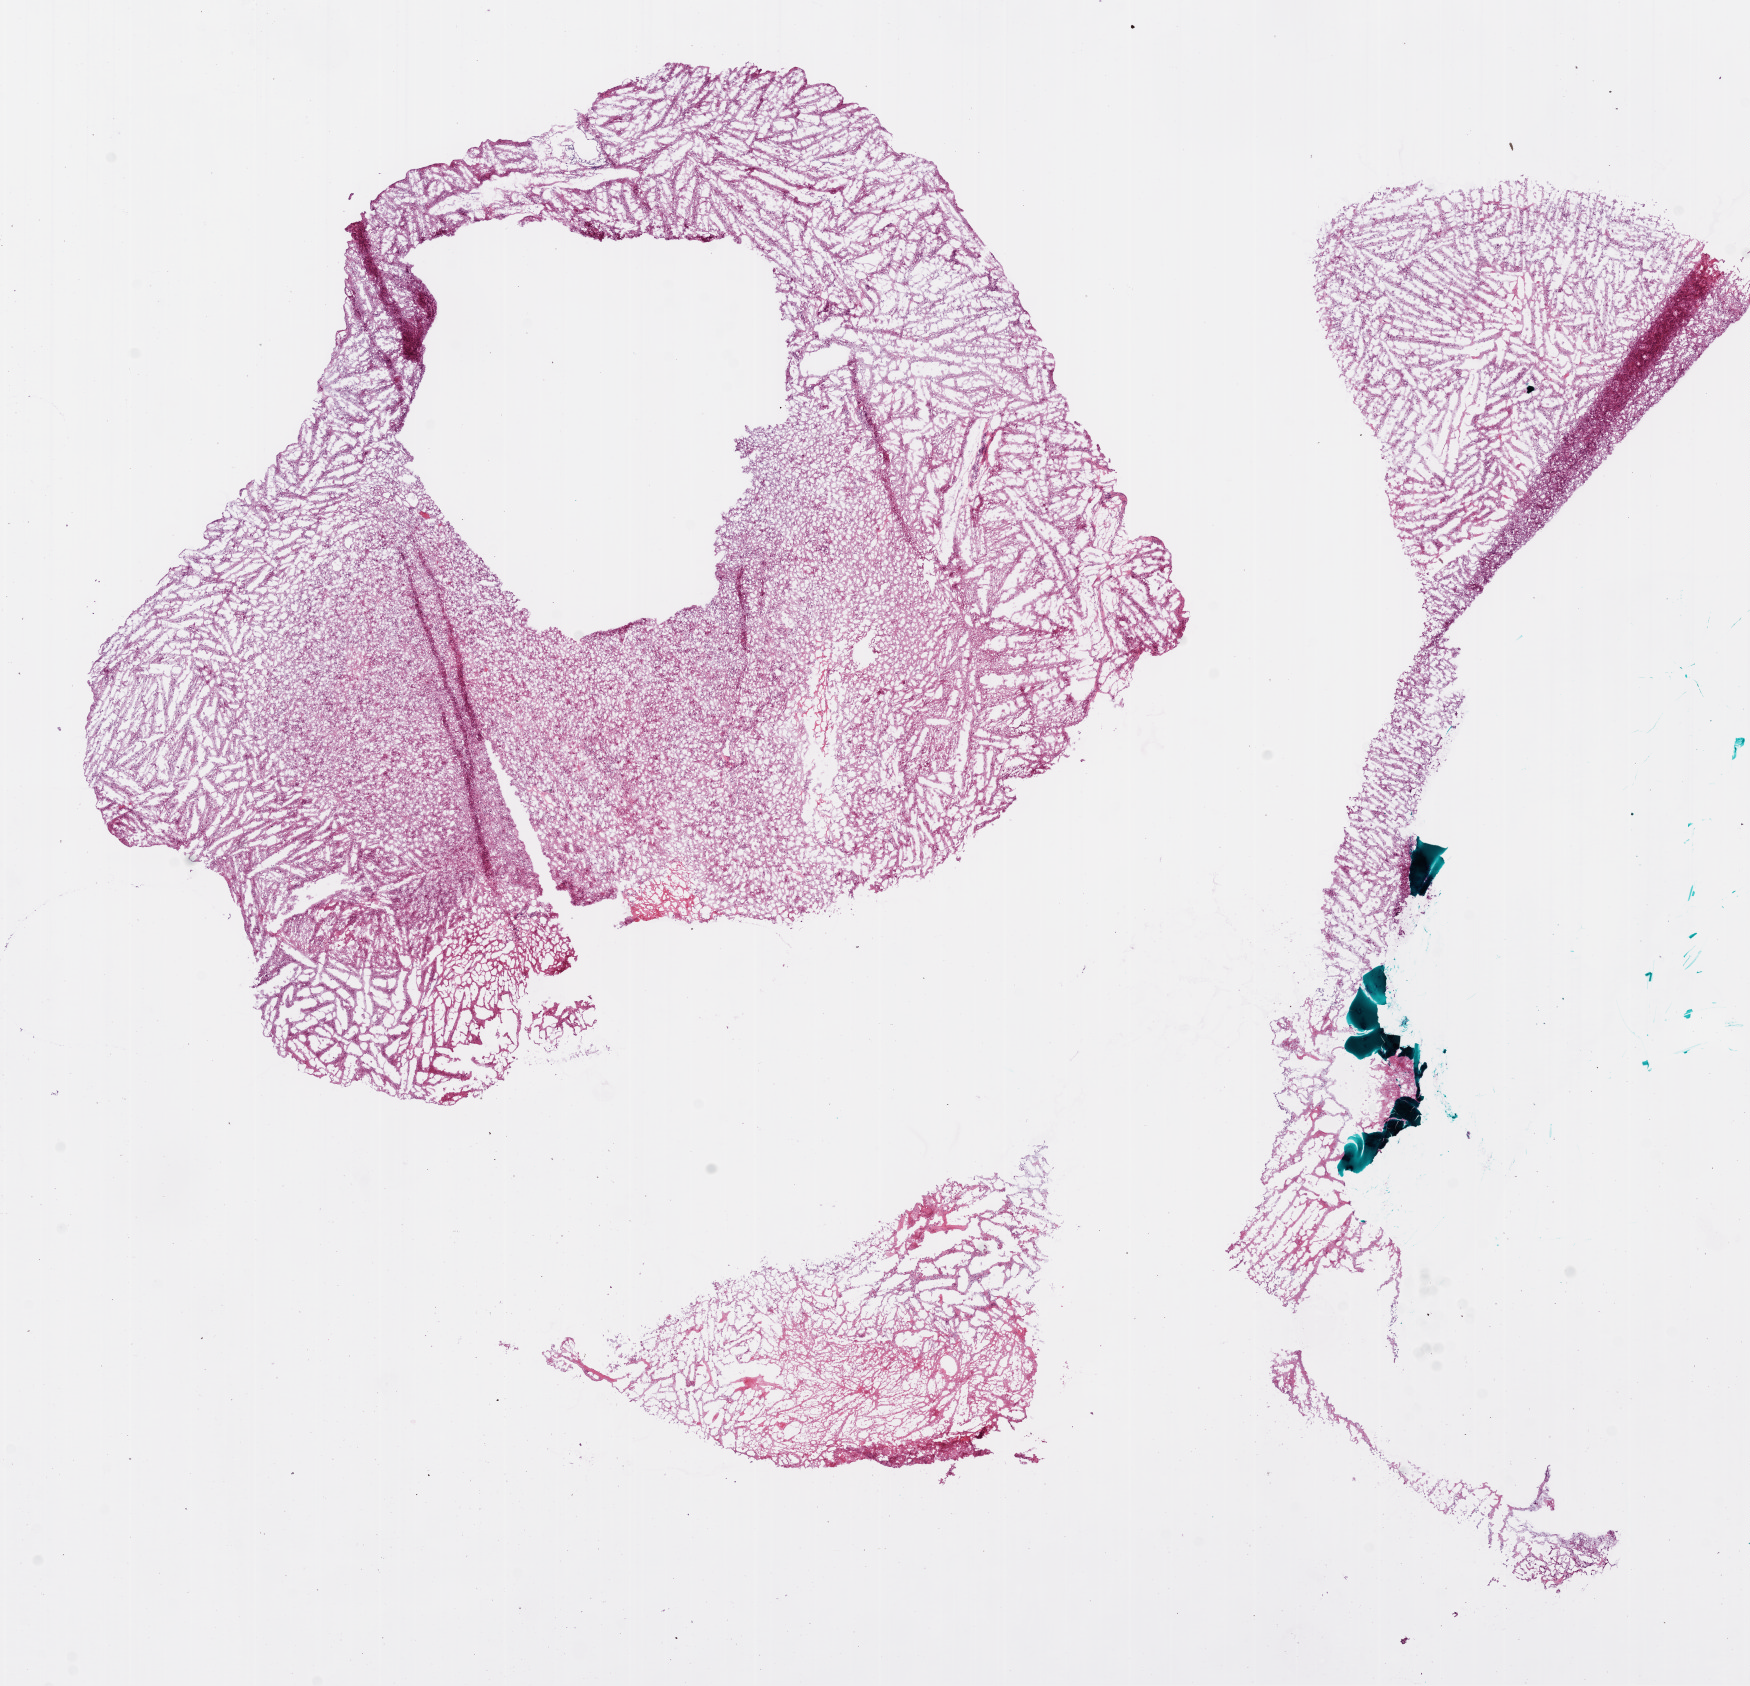
H&E whole-slide image, shown as a low-resolution overview of the whole scanned area (about 14.0 x 13.5 mm, acquisition: 20x scan), frozen section from the bottom of the tissue portion, brain, primary tumour sample. Patient: male, age at initial diagnosis 57 years. Pathologist review of this section (percent, as recorded): tumour cells 80%, tumour nuclei 100%, normal cells 0%, stromal cells 0%, necrosis 20%. Inflammatory infiltration, as recorded: lymphocyte infiltration 0%.
Histologic diagnosis: Glioblastoma.